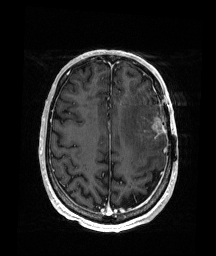
Brain MRI from a brain-tumour surgery series, one axial slice; slice 62 of 176 in the series (ordered by position); T1-weighted post-contrast; 1 mm slice thickness; 216 × 256 image matrix. From the clinical record (not read from this slice): histopathology: Glioblastoma; WHO grade: 4; IDH mutation: no; tumour location: Left Frontal.
Annotated regions visible in this slice (outlined manually by an expert reader):
- tumour: bounding box (x1, y1, x2, y2) in pixels: (138, 115, 165, 144)